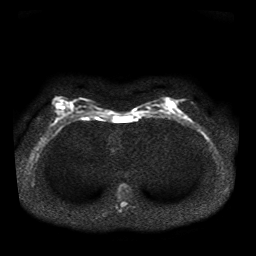
Breast MRI, one axial slice. Slice 20 of 41 in the series (ordered by position). Diffusion-weighted series; image 2 of 4 stored at this slice position (different b-values; order by instance number). 1.5 T. 5 mm slice thickness. 256 × 256 image matrix, field of view 330 × 330 mm. Female patient.
Structures marked on this image (expert manual segmentation):
- tumour on diffusion-weighted imaging: bounding box (x1, y1, x2, y2) in pixels: (183, 115, 189, 120)